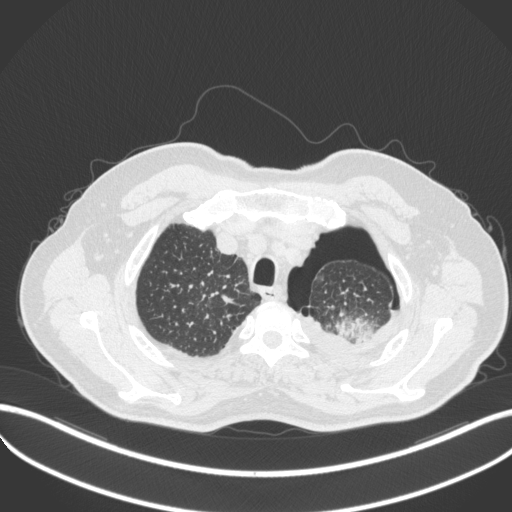
Chest CT, one axial slice; position 422 of 466 along the scan axis; 120 kVp; lung window (W 1500 / L -600 HU); 1 mm slice thickness; 512 × 512 image matrix, field of view 400 × 400 mm. Male patient, age 76 years. Case-level facts recorded for this patient, not image findings: clinical TNM (as recorded): T3 N0 M1b.
Structures marked on this image (bounding box drawn by a radiologist):
- lung tumour (recorded histology: adenocarcinoma): bounding box <333,310,381,345> (left, top, right, bottom; pixels)